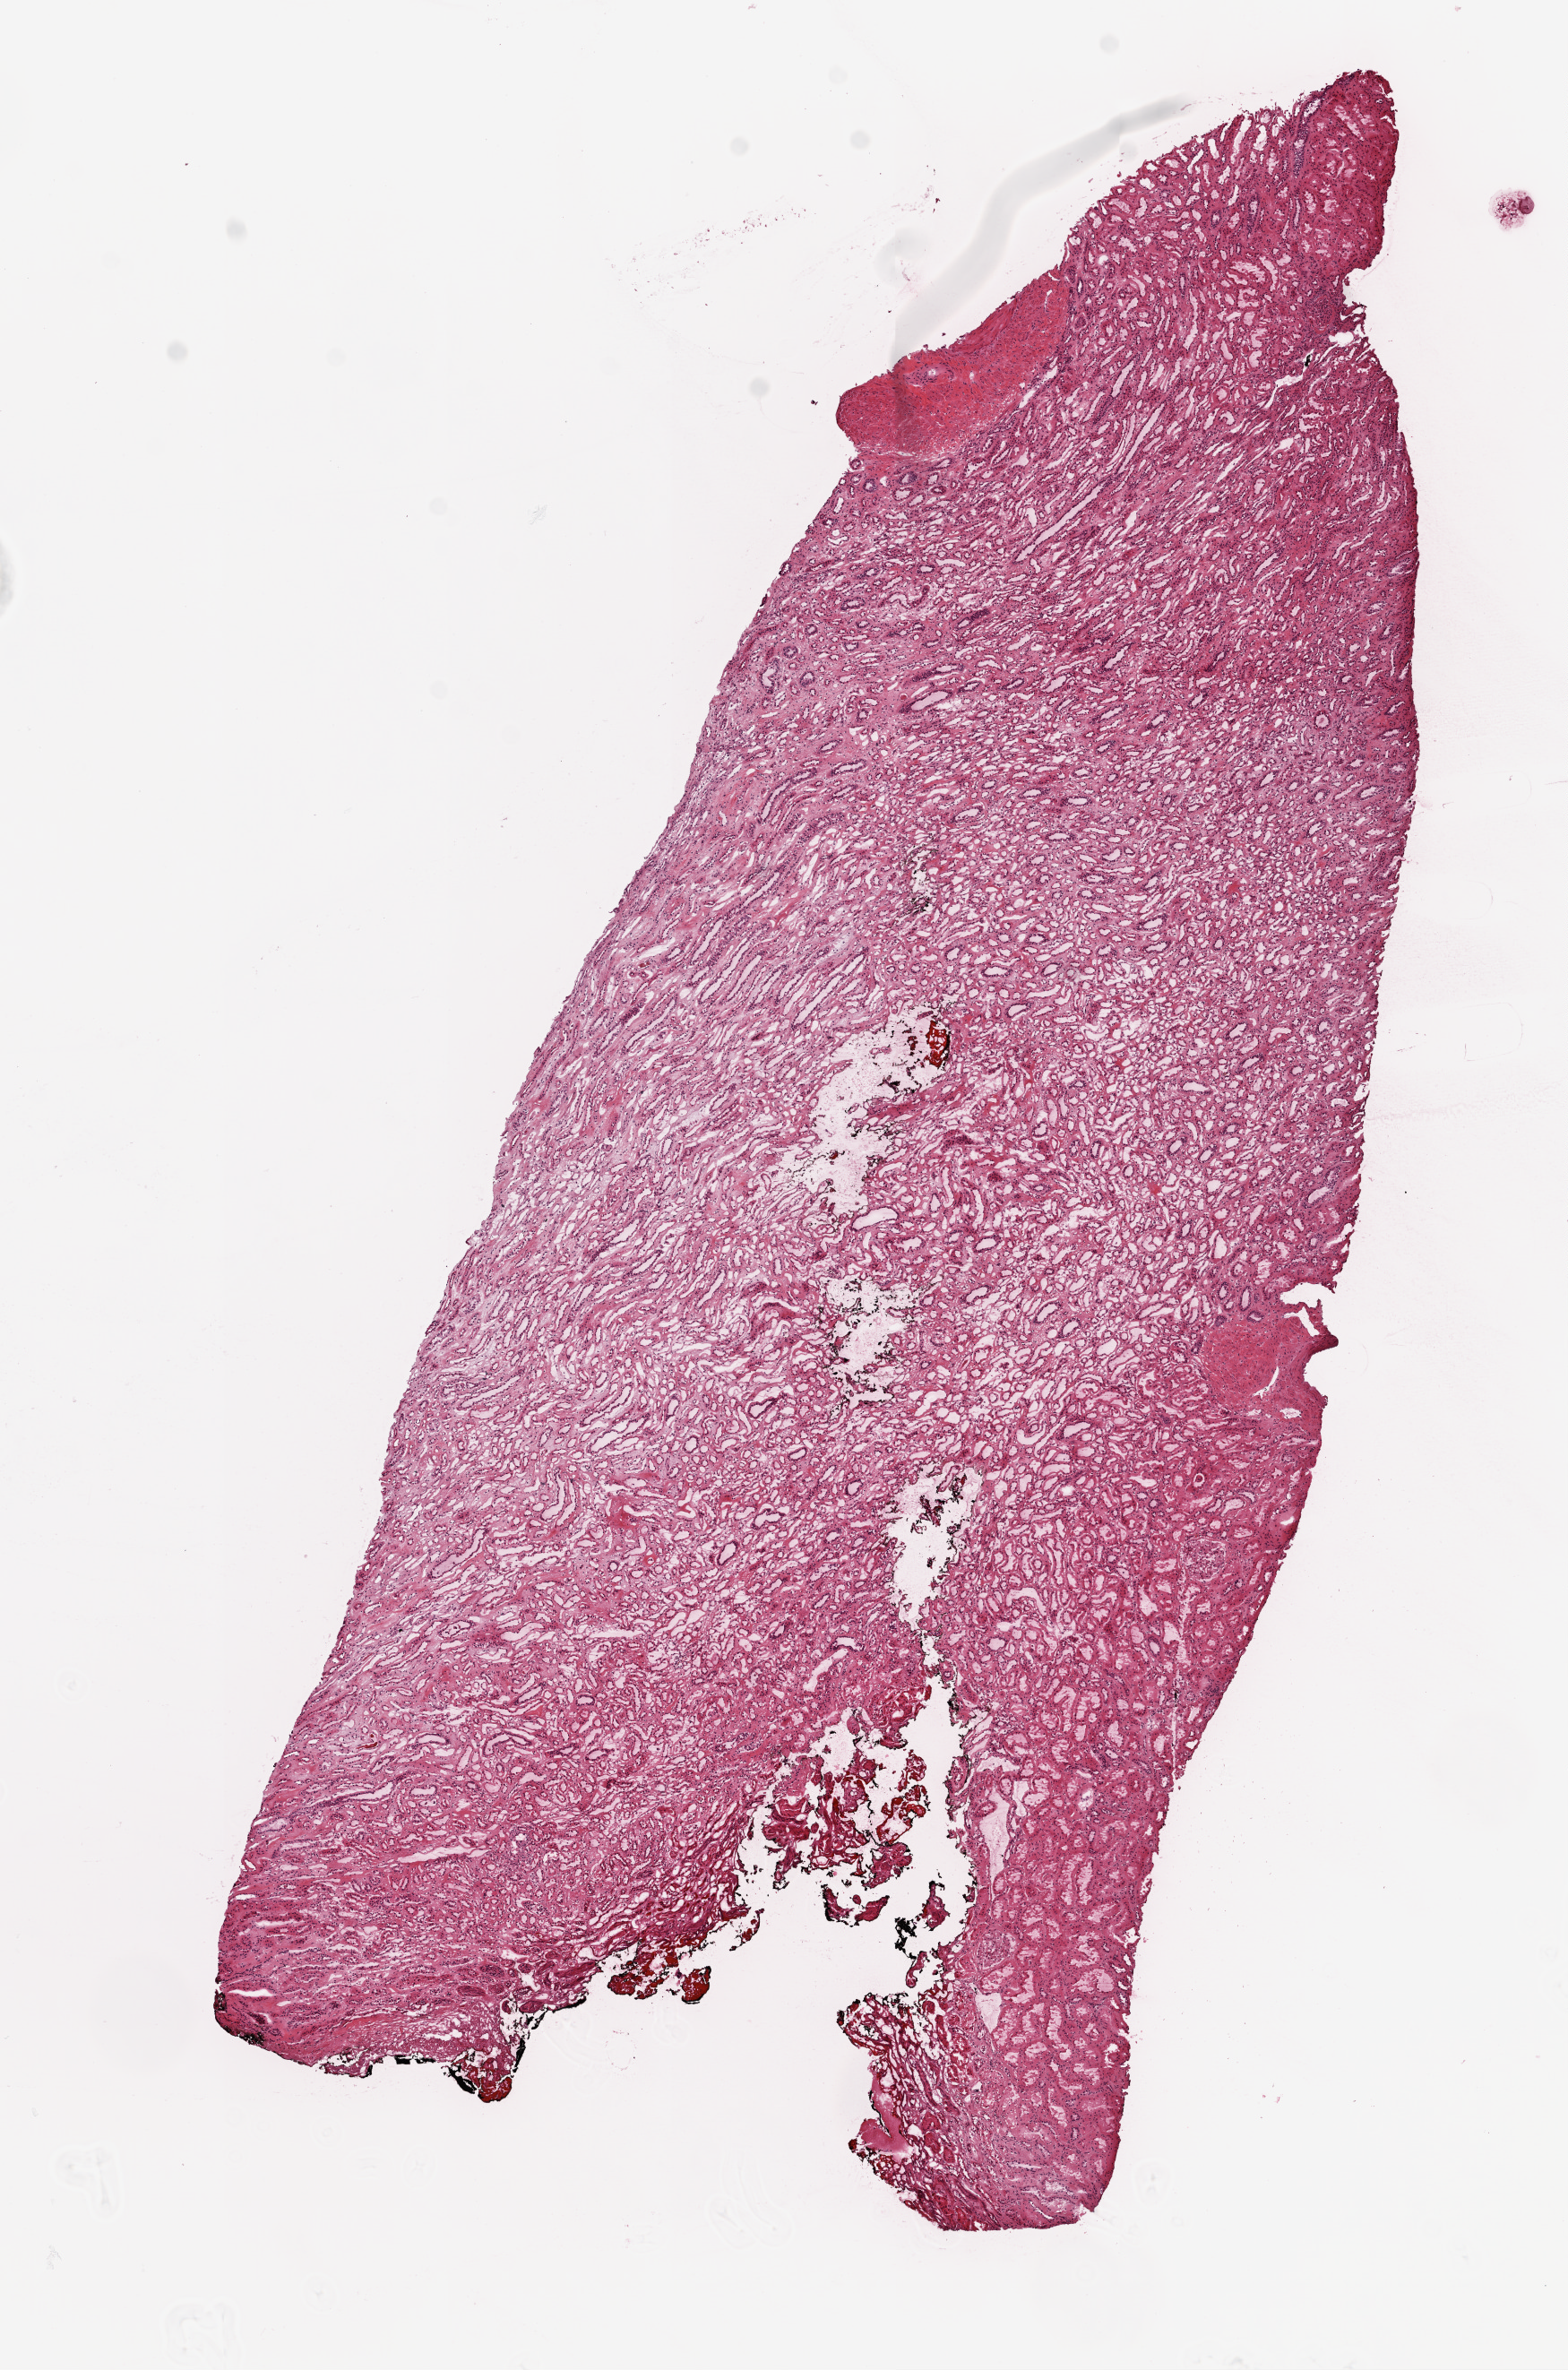
H&E whole-slide image, shown as a low-resolution overview of the whole scanned area (about 7.0 x 10.6 mm), frozen section from the top of the tissue portion, sample: solid tissue normal (non-tumour tissue), kidney. Patient: female, age at initial diagnosis 57 years.
- this section: solid tissue normal sample (biorepository sample class)
- patient diagnosis: Clear cell adenocarcinoma, NOS